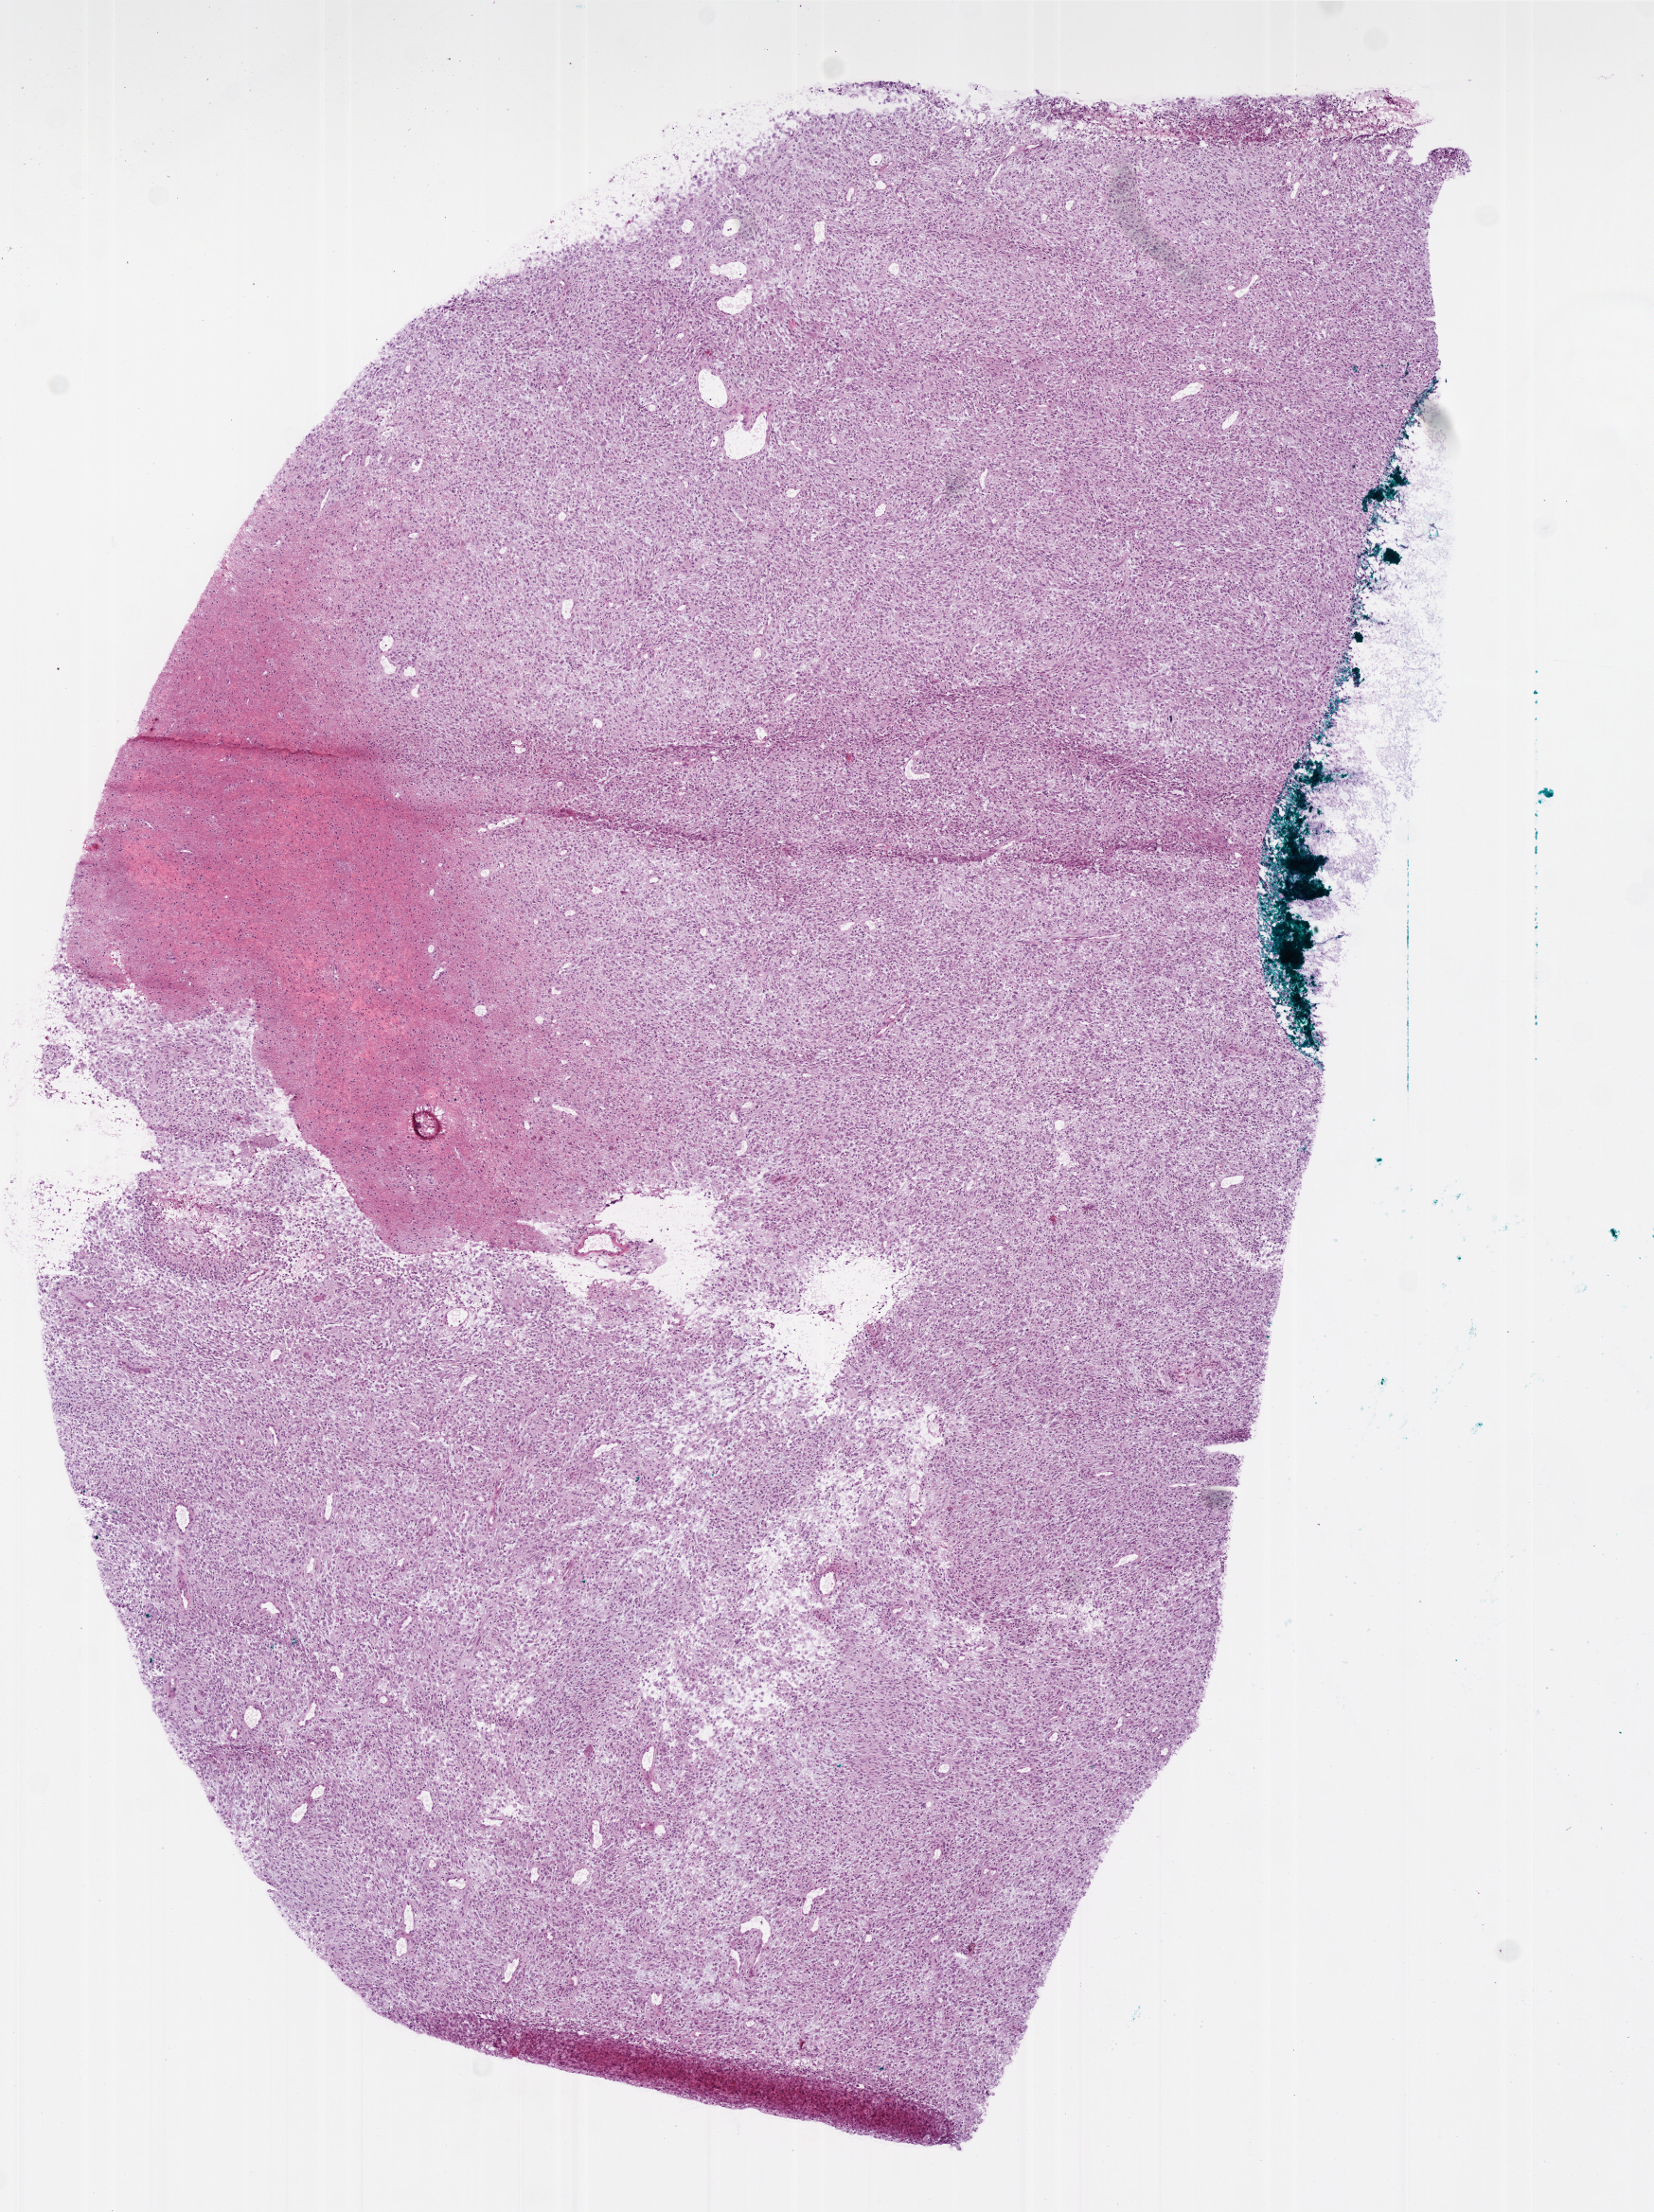
Whole-slide histology image, H&E, shown as a low-resolution overview of the whole scanned area (about 7.0 x 9.4 mm). Frozen section from the bottom of the tissue portion. Primary tumour sample from the brain. Male patient; age at initial diagnosis 69 years. Slide review estimates, as recorded: tumour cells 90%, tumour nuclei 95%, normal cells 0%, stromal cells 5%, necrosis 5%.
Diagnosis: Glioblastoma.